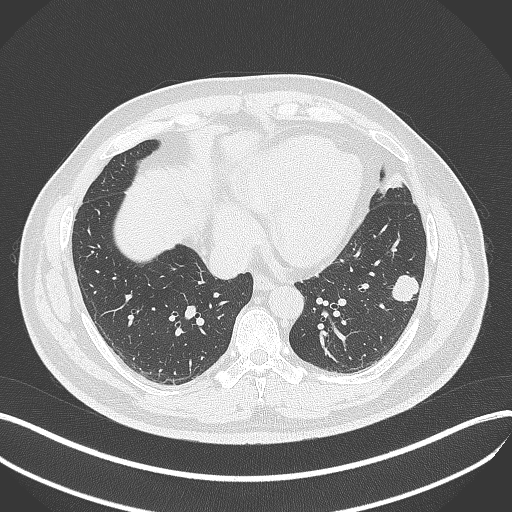
Chest CT, one axial slice. 120 kVp. Lung window (W 1500 / L -600 HU). 512 × 512 image matrix, field of view 400 × 400 mm. Patient: male, 39 years. From the clinical record (not read from this slice): clinical TNM (as recorded): T2a N0 M0.
Outlined on this slice (bounding box drawn by a radiologist):
- lung tumour (recorded histology: adenocarcinoma): bounding box [x1, y1, x2, y2] px = [386, 269, 421, 305]